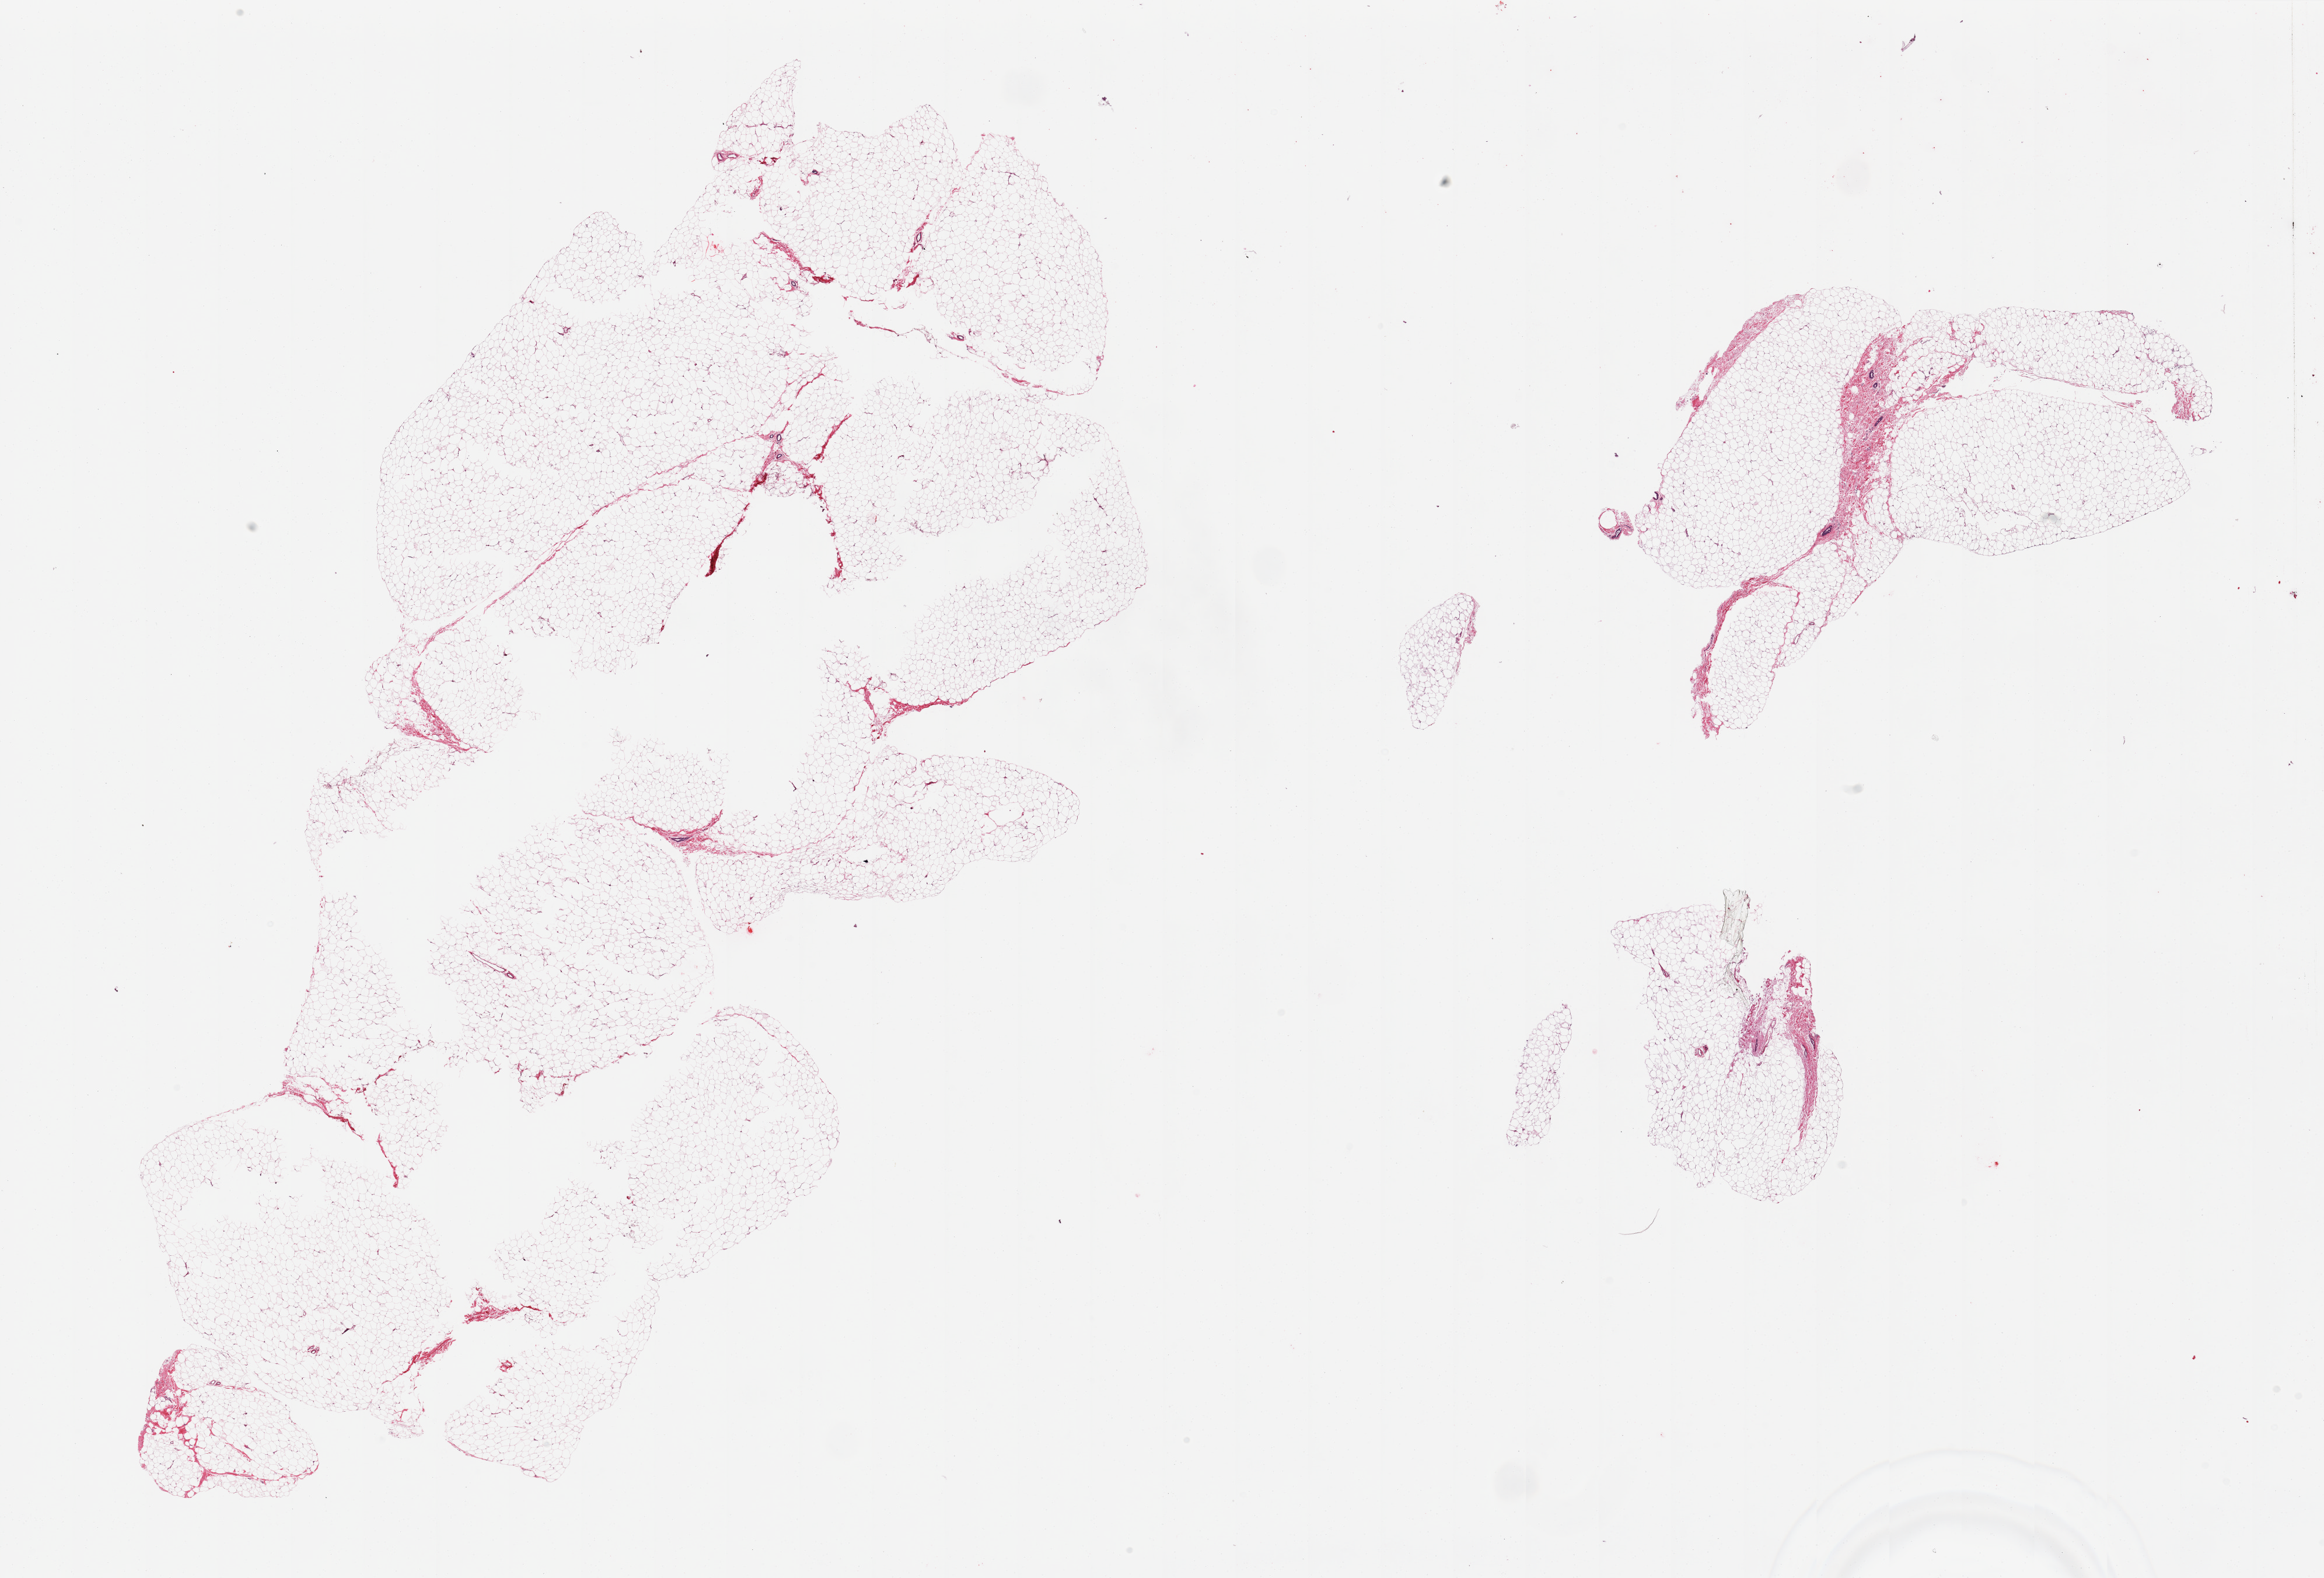
Haematoxylin and eosin whole-slide image, a low-resolution overview of the entire scanned area, about 31.5 x 21.4 mm.
- specimen: PAXgene-fixed paraffin-embedded (PFPE) section; target tissue: breast; donor tissue sample